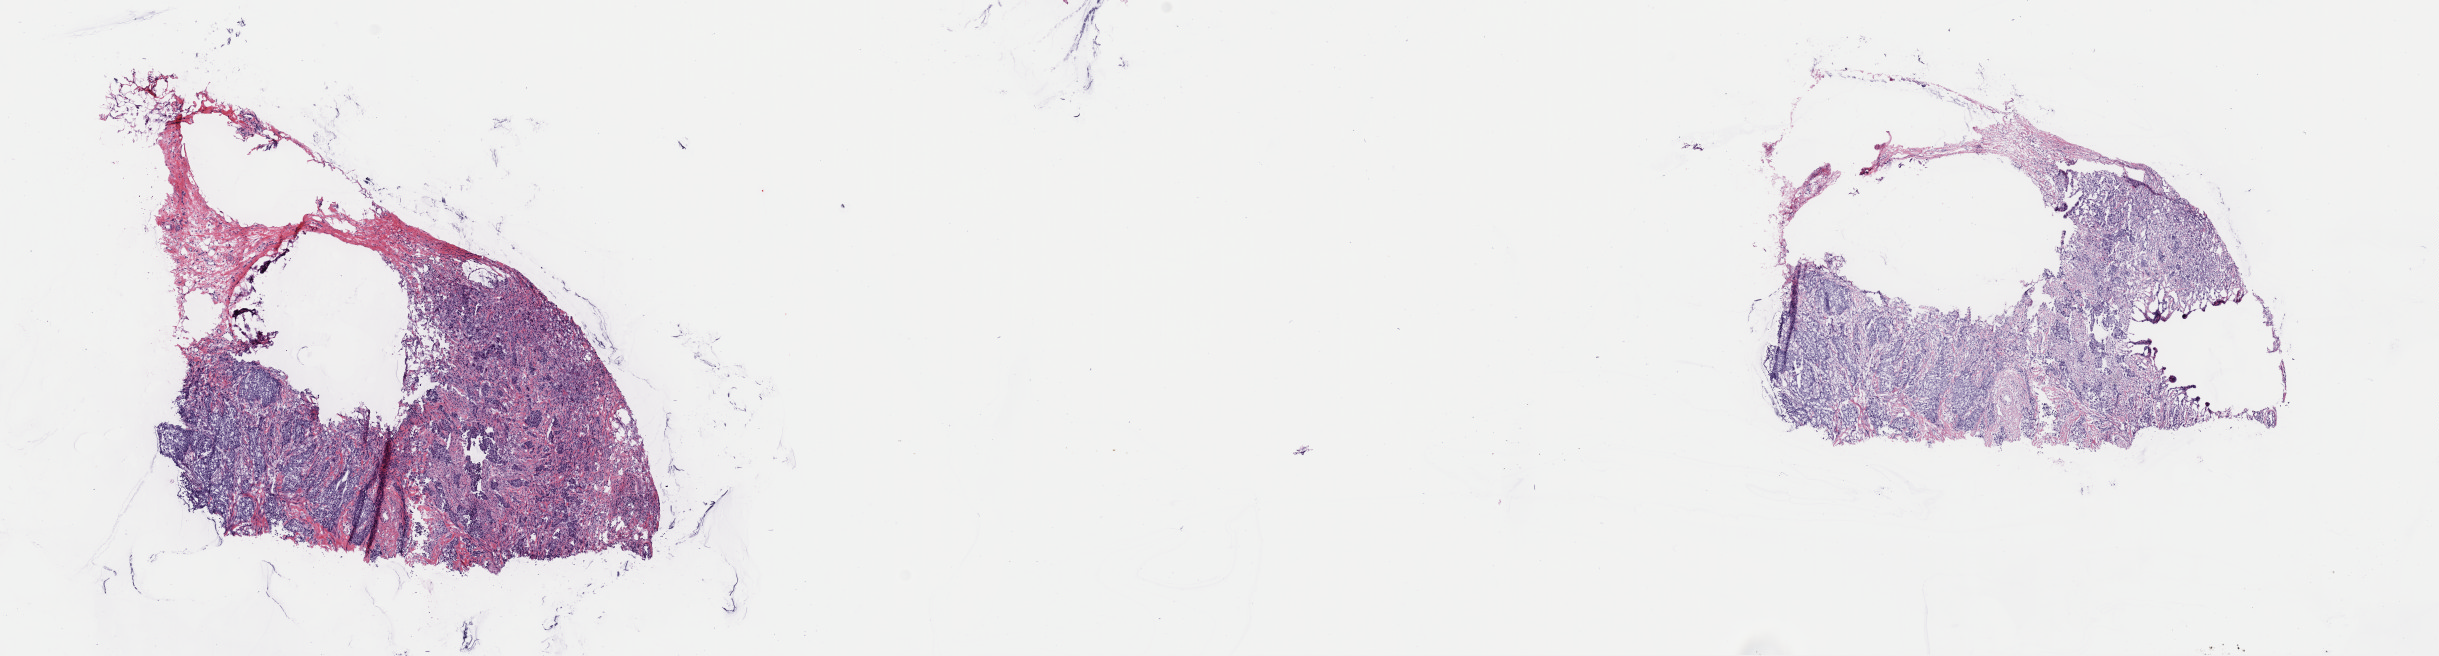
Whole-slide histology image, H&E-stained, low-resolution overview of the scanned area, about 19.3 x 5.2 mm (from a 40x scan). Frozen section from the top of the tissue portion. Sample: primary tumour, breast. Female patient; age at initial diagnosis 51 years. Pathologist review of this section (percent, as recorded): tumour cells 50%, tumour nuclei 85%, normal cells 0%, stromal cells 49%, necrosis 1%. Inflammatory infiltration, as recorded: lymphocyte infiltration 8%, monocyte infiltration 2%, neutrophil infiltration 0%.
• pathologic diagnosis: Infiltrating duct carcinoma, NOS
• AJCC pathologic stage: IIA
• TNM: T2 N0 M0